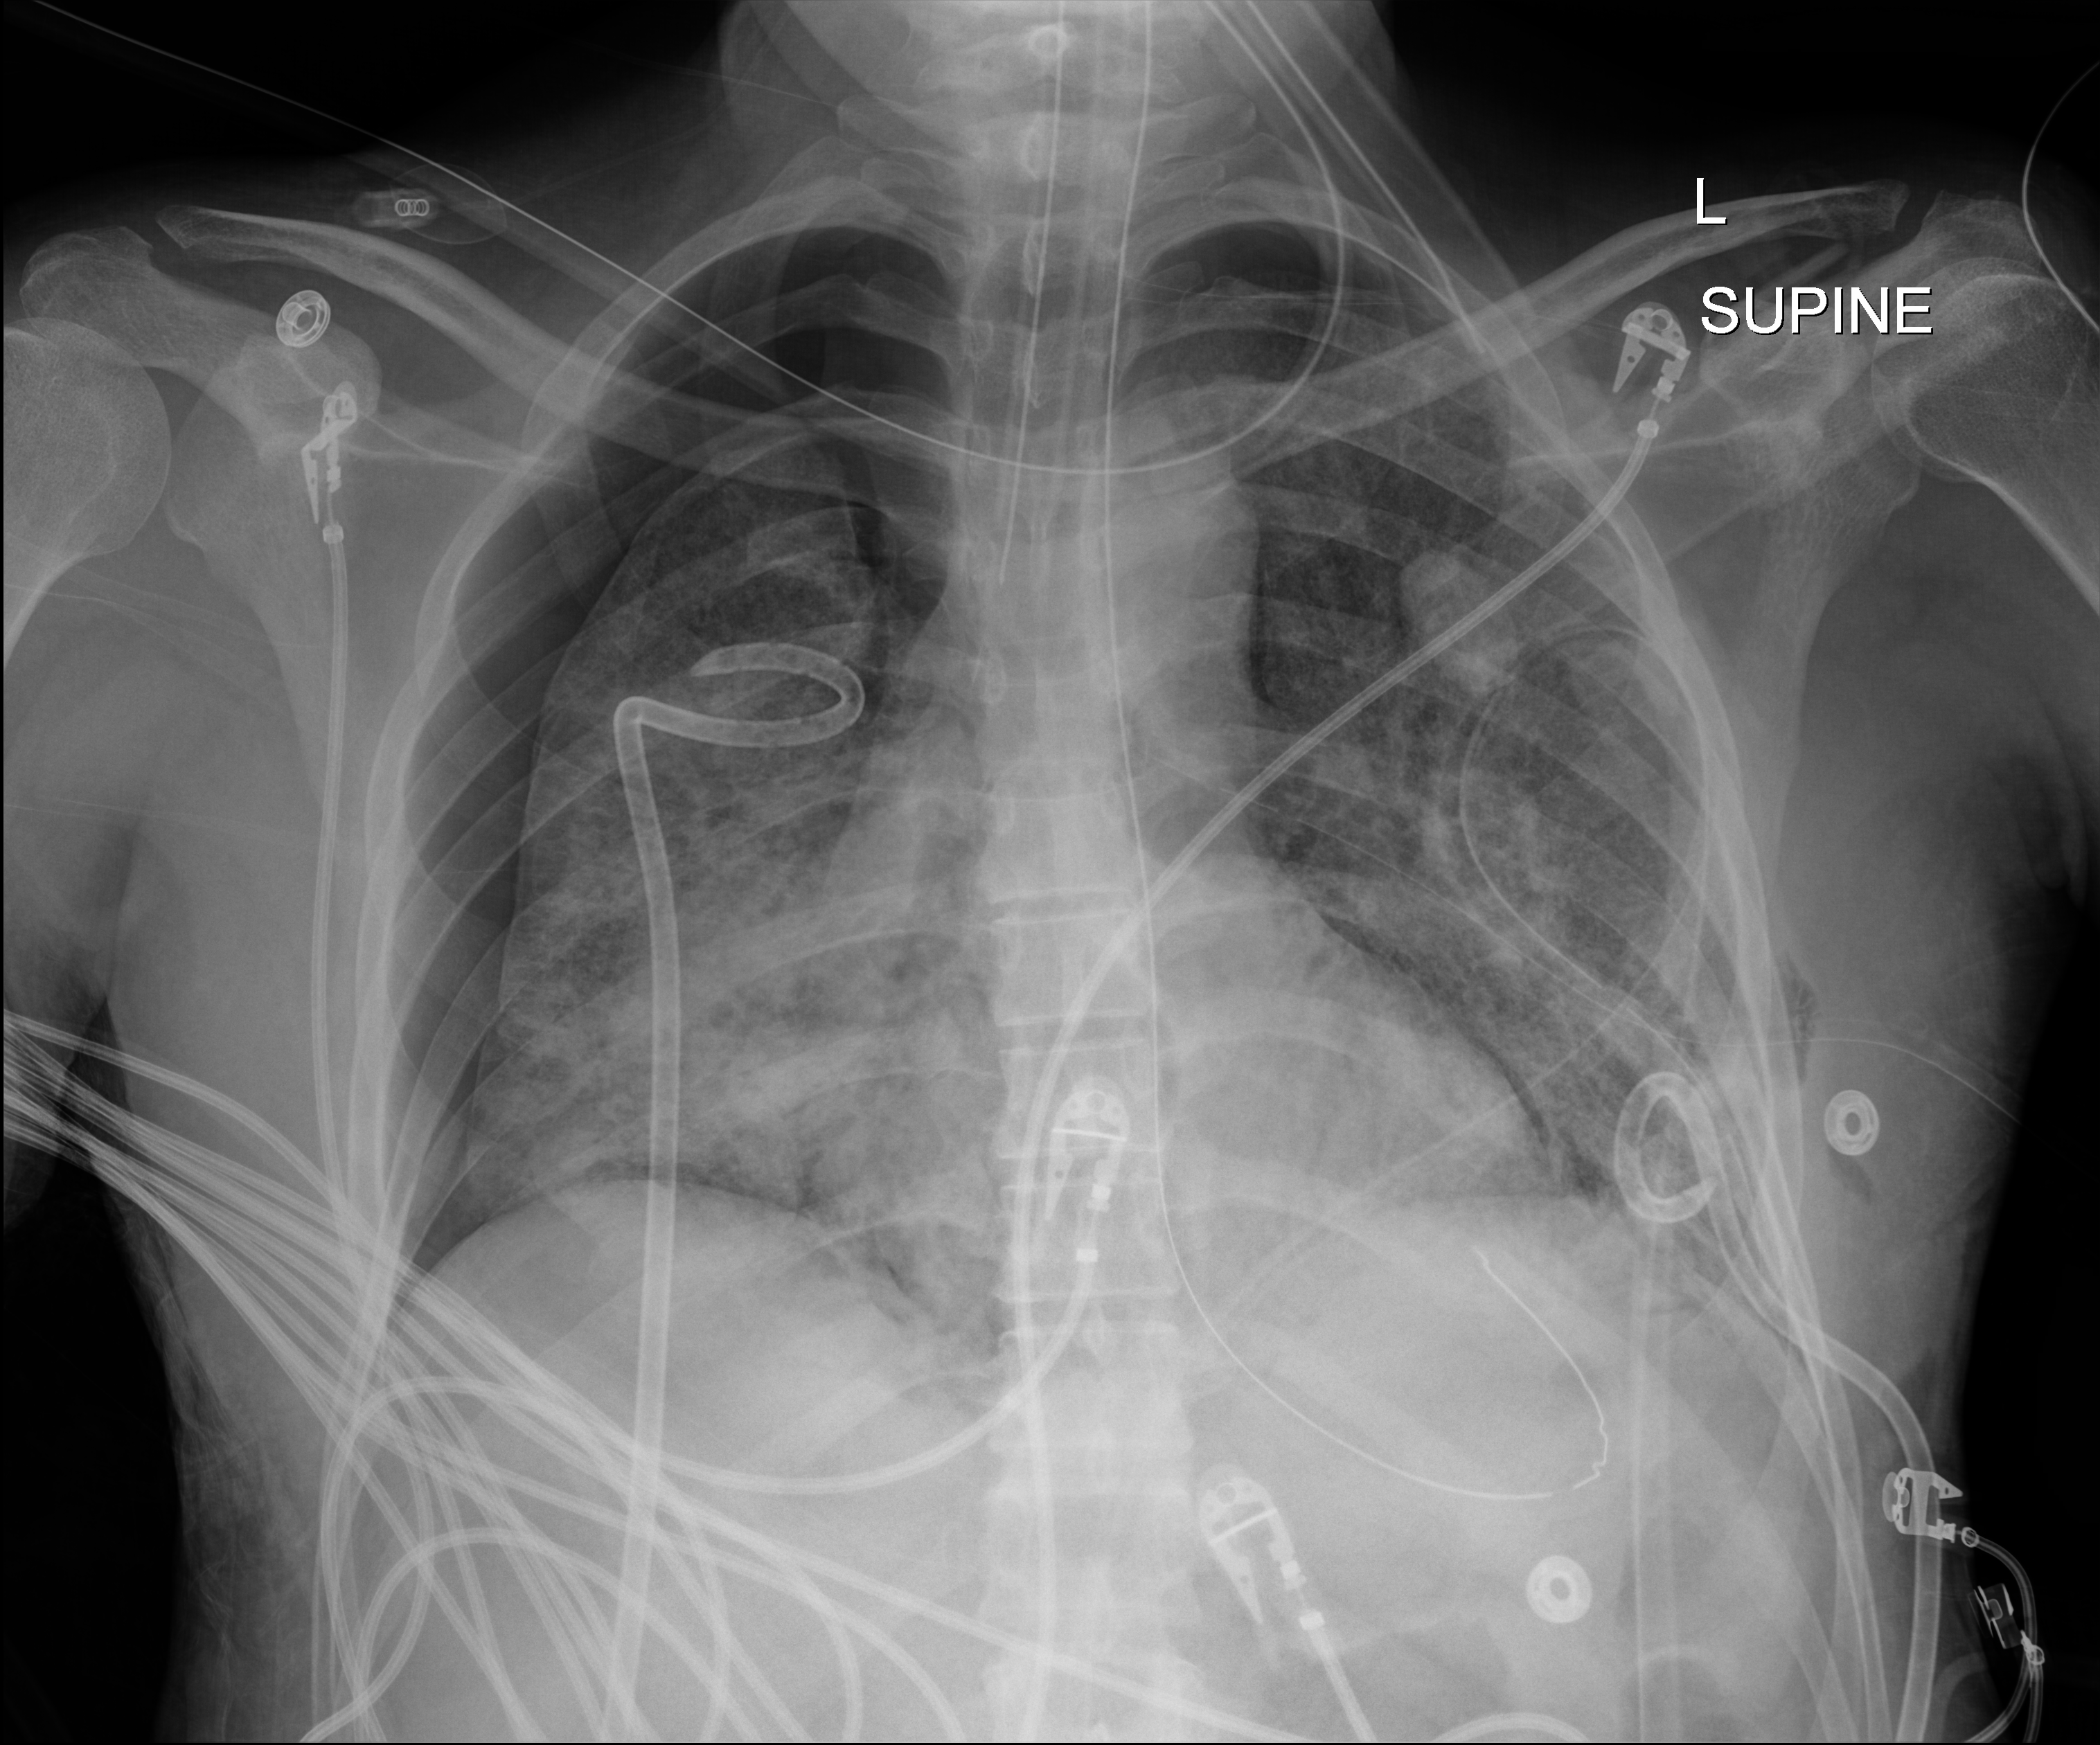
Chest radiograph (digital radiography), anteroposterior (AP) projection. Patient hospitalised with COVID-19, aged 18–59 years.
From the hospital-stay record, not from the radiograph (when in the stay this image was taken is not recorded): other chronic lung disease (admission record): no; length of hospital stay: 41 days.